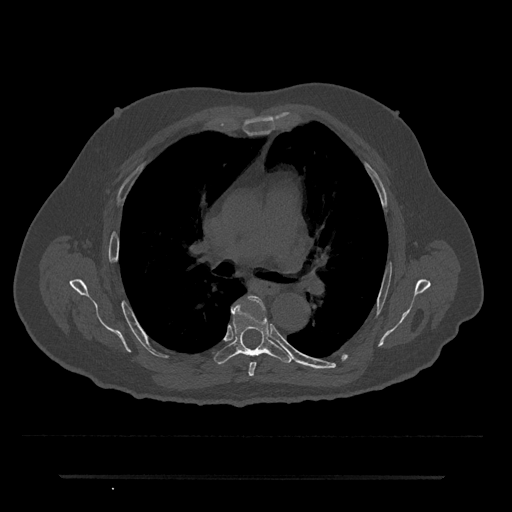
CT including the spine, one axial slice. Slice 450 of 797 in the series (ordered by position). 120 kVp. Bone window (W 1800 / L 400 HU). 0.5 mm slice thickness. 512 × 512 image matrix. Patient: male, 69 years. Case-level facts recorded for this patient, not image findings: primary cancer: prostate.
Annotated regions visible in this slice (semi-automatic segmentation, software-assisted and operator-edited):
- T5 vertebra: bounding box <248,296,264,376> (left, top, right, bottom; pixels)
- T6 vertebra: <214,301,293,364>